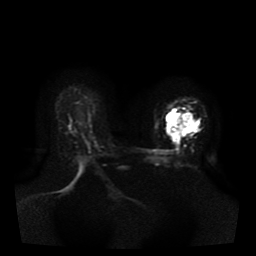
Breast MRI, one axial slice. Diffusion-weighted series; image 2 of 4 stored at this slice position (different b-values; order by instance number). 1.5 T. 256 × 256 image matrix. Female patient.
Outlined on this slice (manually delineated by an expert):
- tumour on diffusion-weighted imaging: bounding box <167,113,195,142> (left, top, right, bottom; pixels)